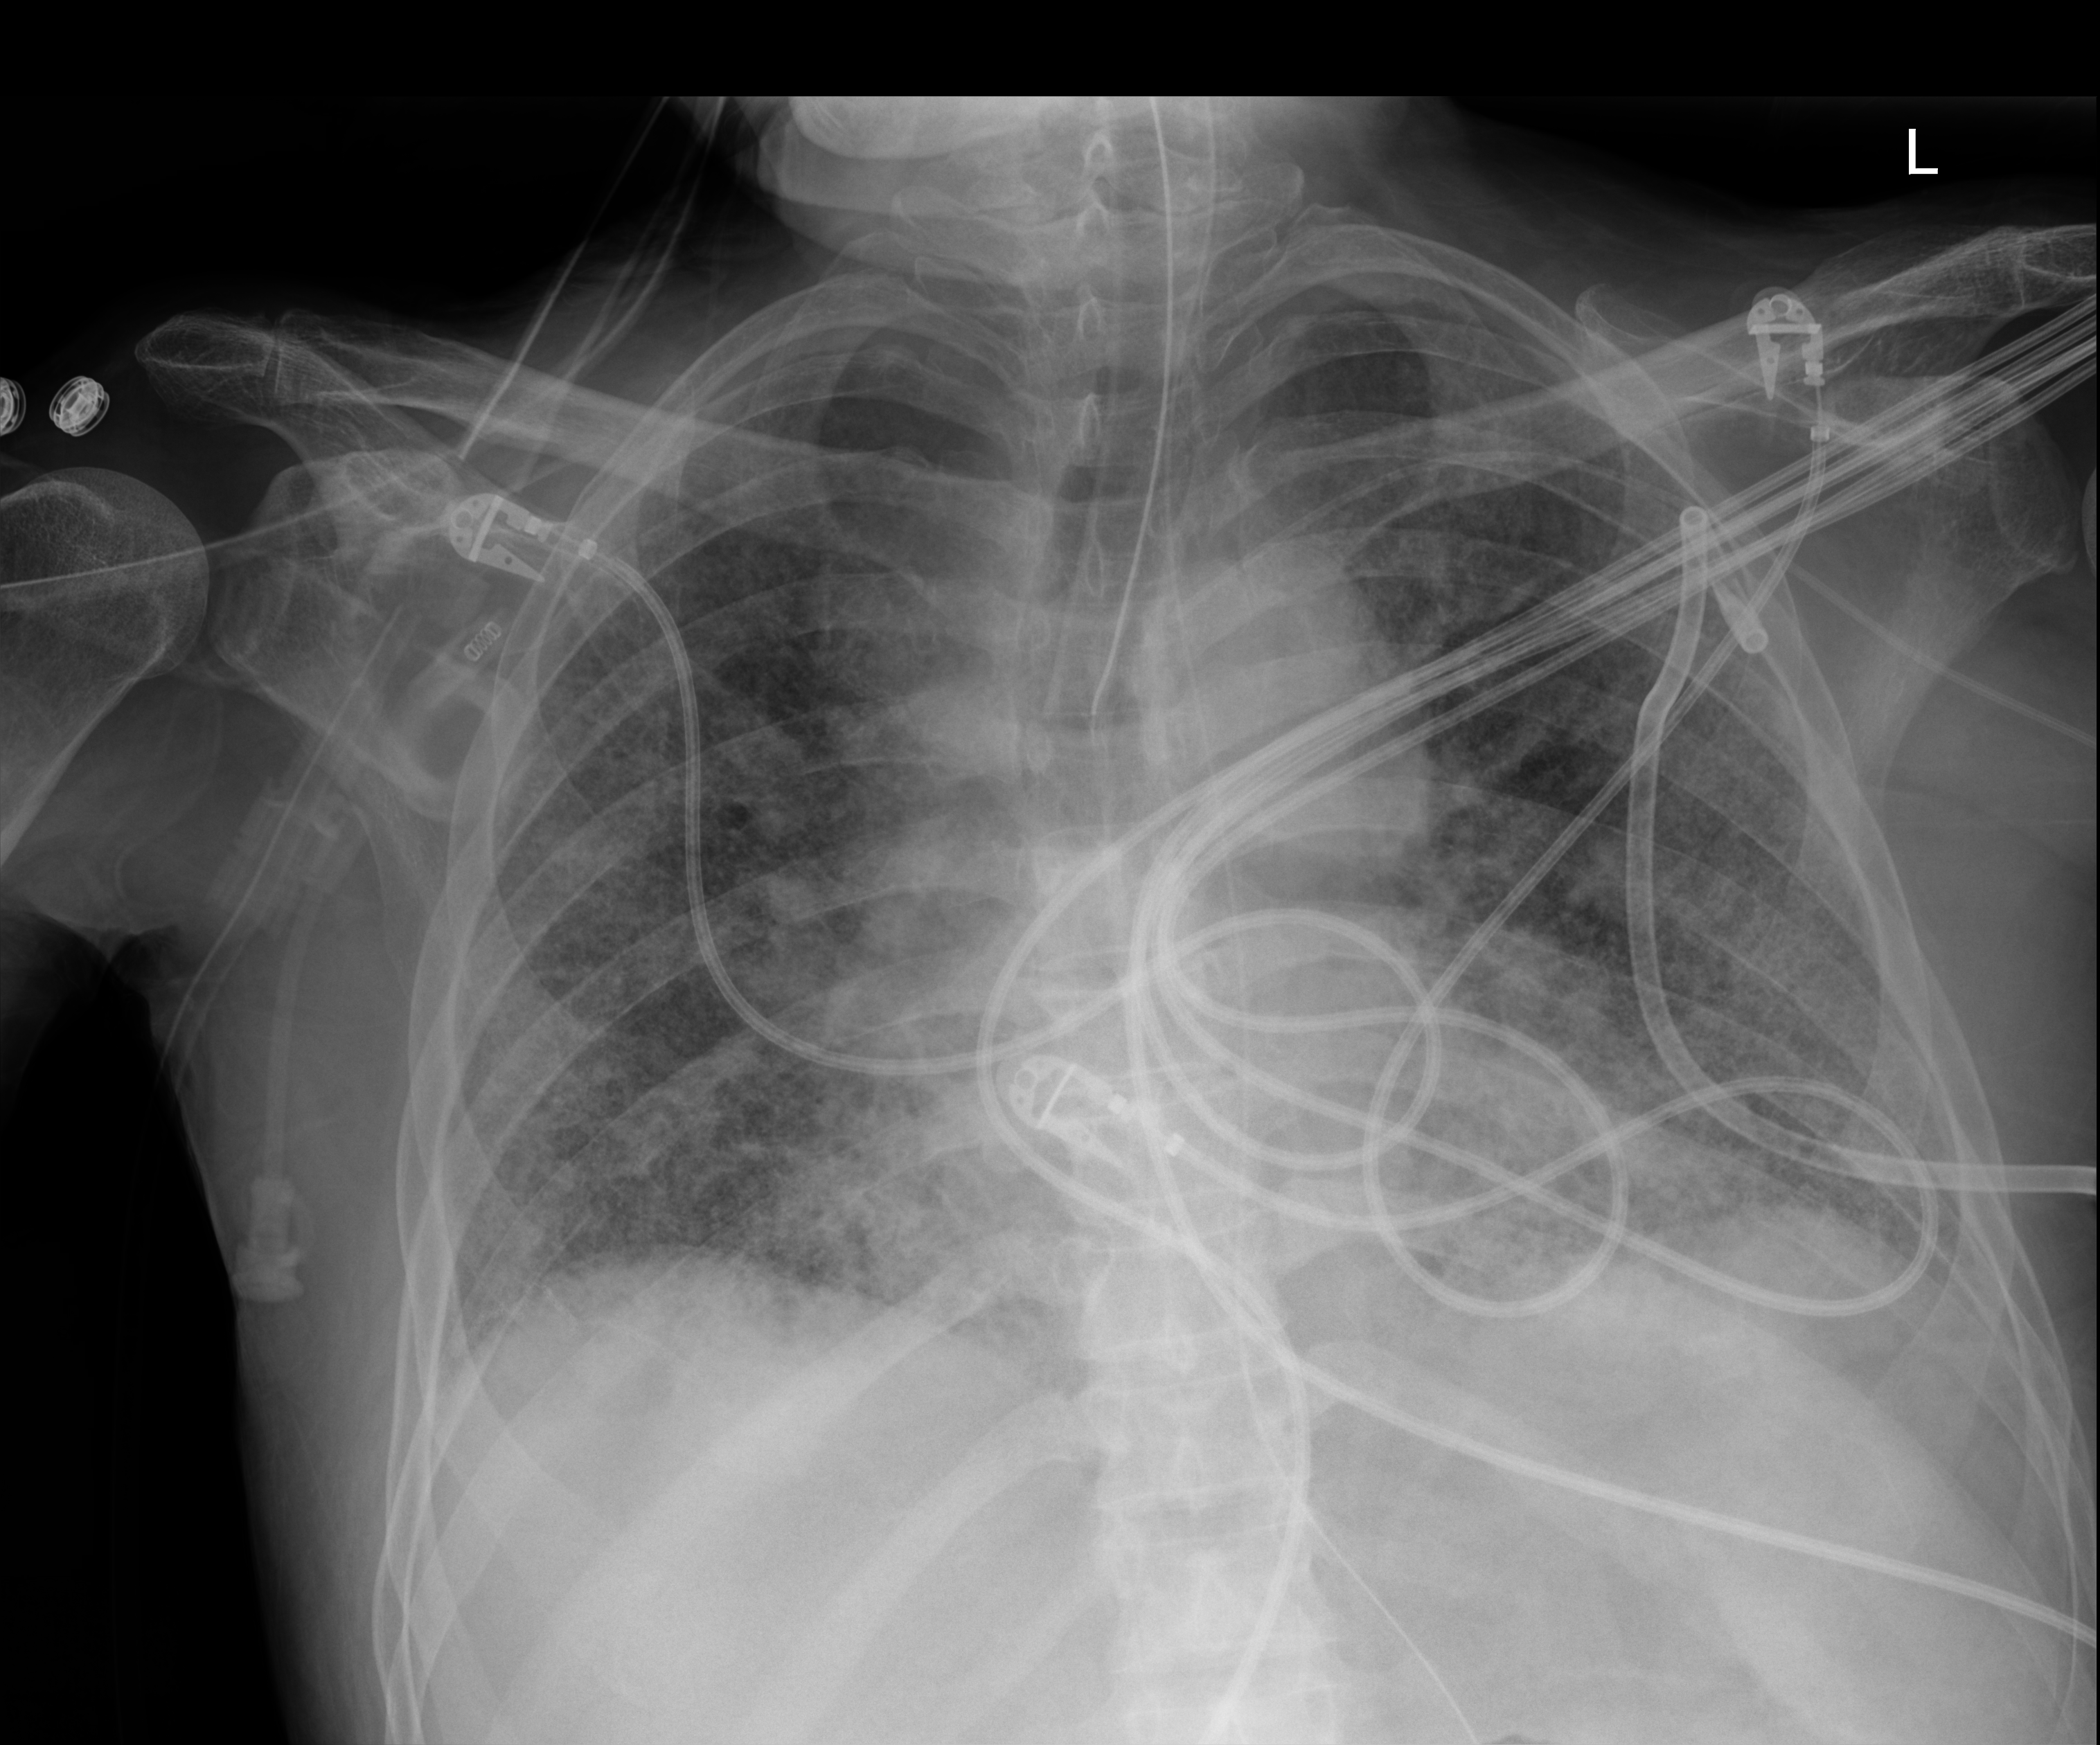
Chest radiograph (digital radiography), anteroposterior (AP) projection. Patient hospitalised with COVID-19; male, aged 60–74 years.
From the hospital-stay record, not from the radiograph (when in the stay this image was taken is not recorded): mechanically ventilated during this hospital stay: yes.